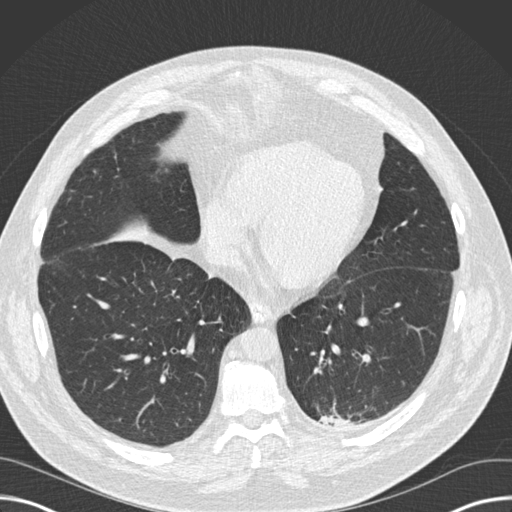
Low-dose screening chest CT, one axial slice. Position 55 of 160 along the scan axis. Reconstruction kernel B30f. Lung window (W 1500 / L -600 HU). 2 mm slice thickness. 512 × 512 image matrix, field of view 382 × 382 mm.
Structures marked on this image (expert manual segmentation):
- lesion 1 (tumor, upper lobe of left lung): bounding box [x1, y1, x2, y2] px = [320, 415, 348, 426]